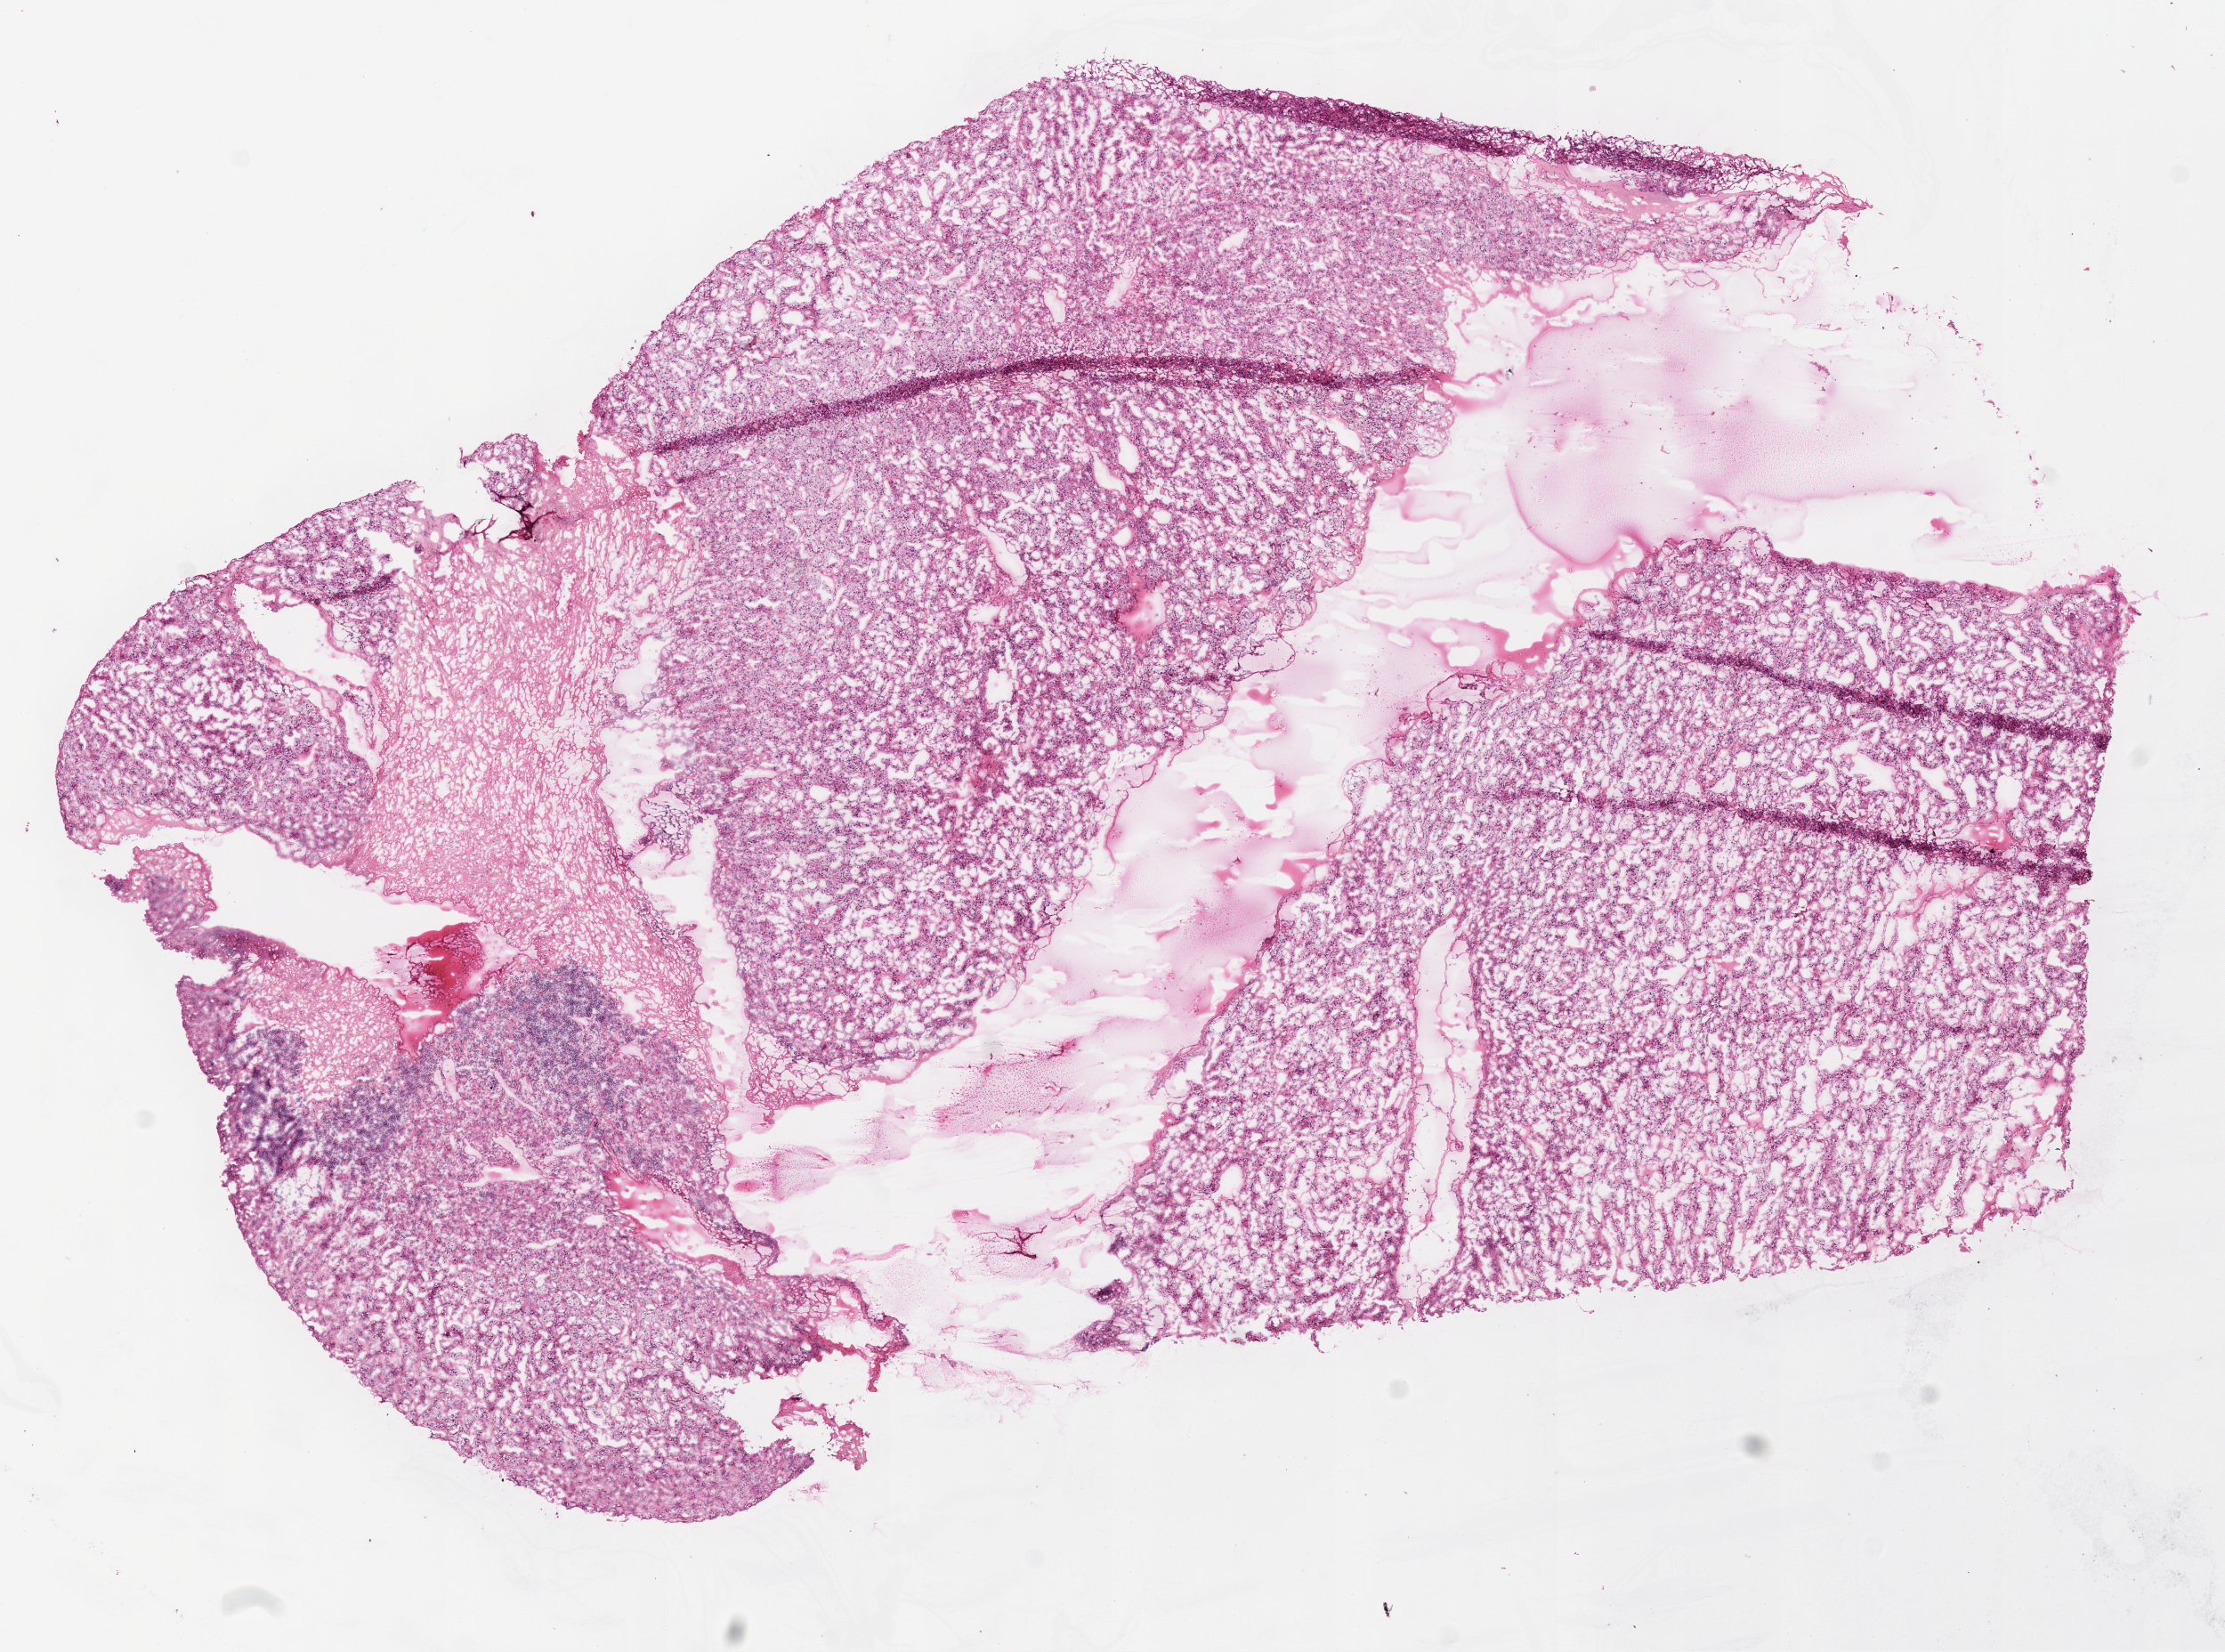
Whole-slide histology image, Hematoxylin and eosin (H&E) stained, a low-resolution overview of the entire scanned area, about 10.0 x 7.4 mm (slide scanned at 20x), frozen section from the top of the tissue portion, primary tumour sample from the kidney. Female patient; age at initial diagnosis 54 years. Histologic grade: G2 (moderately differentiated). Pathologist review of this section (percent, as recorded): tumour cells 85%, tumour nuclei 80%, normal cells 0%, stromal cells 15%, necrosis 0%.
AJCC pathologic stage: II (7th edition). Diagnosis: Clear cell adenocarcinoma, NOS. Laterality: right. Lymph nodes positive (case pathology): 0 of 5 examined. TNM: T2 N0 M0.